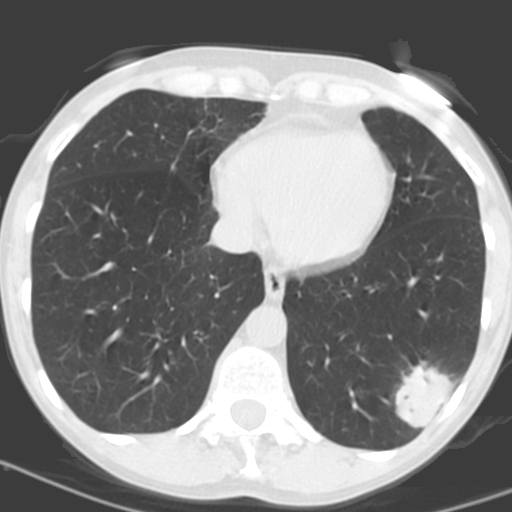
Low-dose screening chest CT, one axial slice; position 50 of 156 along the scan axis; 120 kVp; lung window (W 1500 / L -600 HU); 3.2 mm slice thickness; 512 × 512 image matrix, field of view 262 × 262 mm.
Annotated regions visible in this slice (expert manual segmentation):
- lesion 1 (tumor, lower lobe of left lung): bounding box (x1, y1, x2, y2) in pixels: (396, 361, 456, 429)